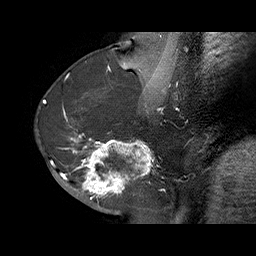
Breast MRI (dynamic contrast-enhanced), one sagittal slice; dynamic contrast-enhanced series, time point 2 of 6 at this slice position (early post-contrast); 1.5 T; TE 4.5 ms, TR 32.4 ms; 3 mm slice thickness; 256 × 256 image matrix, field of view 180 × 180 mm. Female patient. From the clinical record (not read from this slice): setting: breast cancer imaged before/during neoadjuvant chemotherapy; receptor status: HR-positive, HER2-negative.
Structures marked on this image (semi-automatically segmented with operator editing):
- analysis volume of interest (the breast-tissue region the enhancement analysis was run in; not a lesion): bounding box [x1, y1, x2, y2] px = [71, 128, 159, 202]
- tumour enhancement mask (voxels above the 100 % enhancement threshold inside the analysis volume of interest): [71, 132, 152, 199]